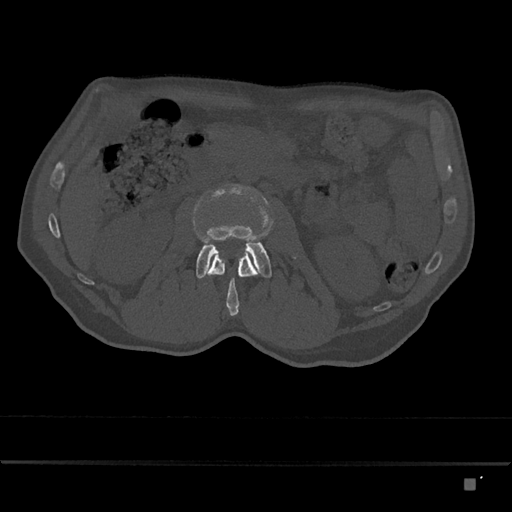
CT including the spine, one axial slice; position 439 of 797 along the scan axis; bone window (W 1800 / L 400 HU); 0.5 mm slice thickness; 512 × 512 image matrix, field of view 390 × 390 mm. Male patient, age 72 years. Case-level facts recorded for this patient, not image findings: primary cancer: prostate.
Annotated regions visible in this slice (semi-automatically segmented with operator editing):
- L2 vertebra: bounding box <204,248,258,316> (left, top, right, bottom; pixels)
- L3 vertebra: <196,184,272,278>